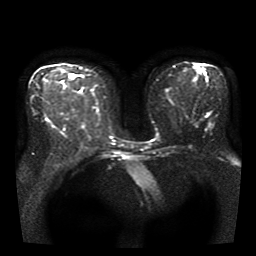
Breast MRI, one axial slice. Position 18 of 41 along the scan axis. Diffusion-weighted series; image 2 of 4 stored at this slice position (different b-values; order by instance number). 1.5 T. 5 mm slice thickness. 256 × 256 image matrix, field of view 330 × 330 mm. Female patient.
Structures marked on this image (expert manual segmentation):
- tumour on diffusion-weighted imaging: bounding box <71,75,74,77> (left, top, right, bottom; pixels)